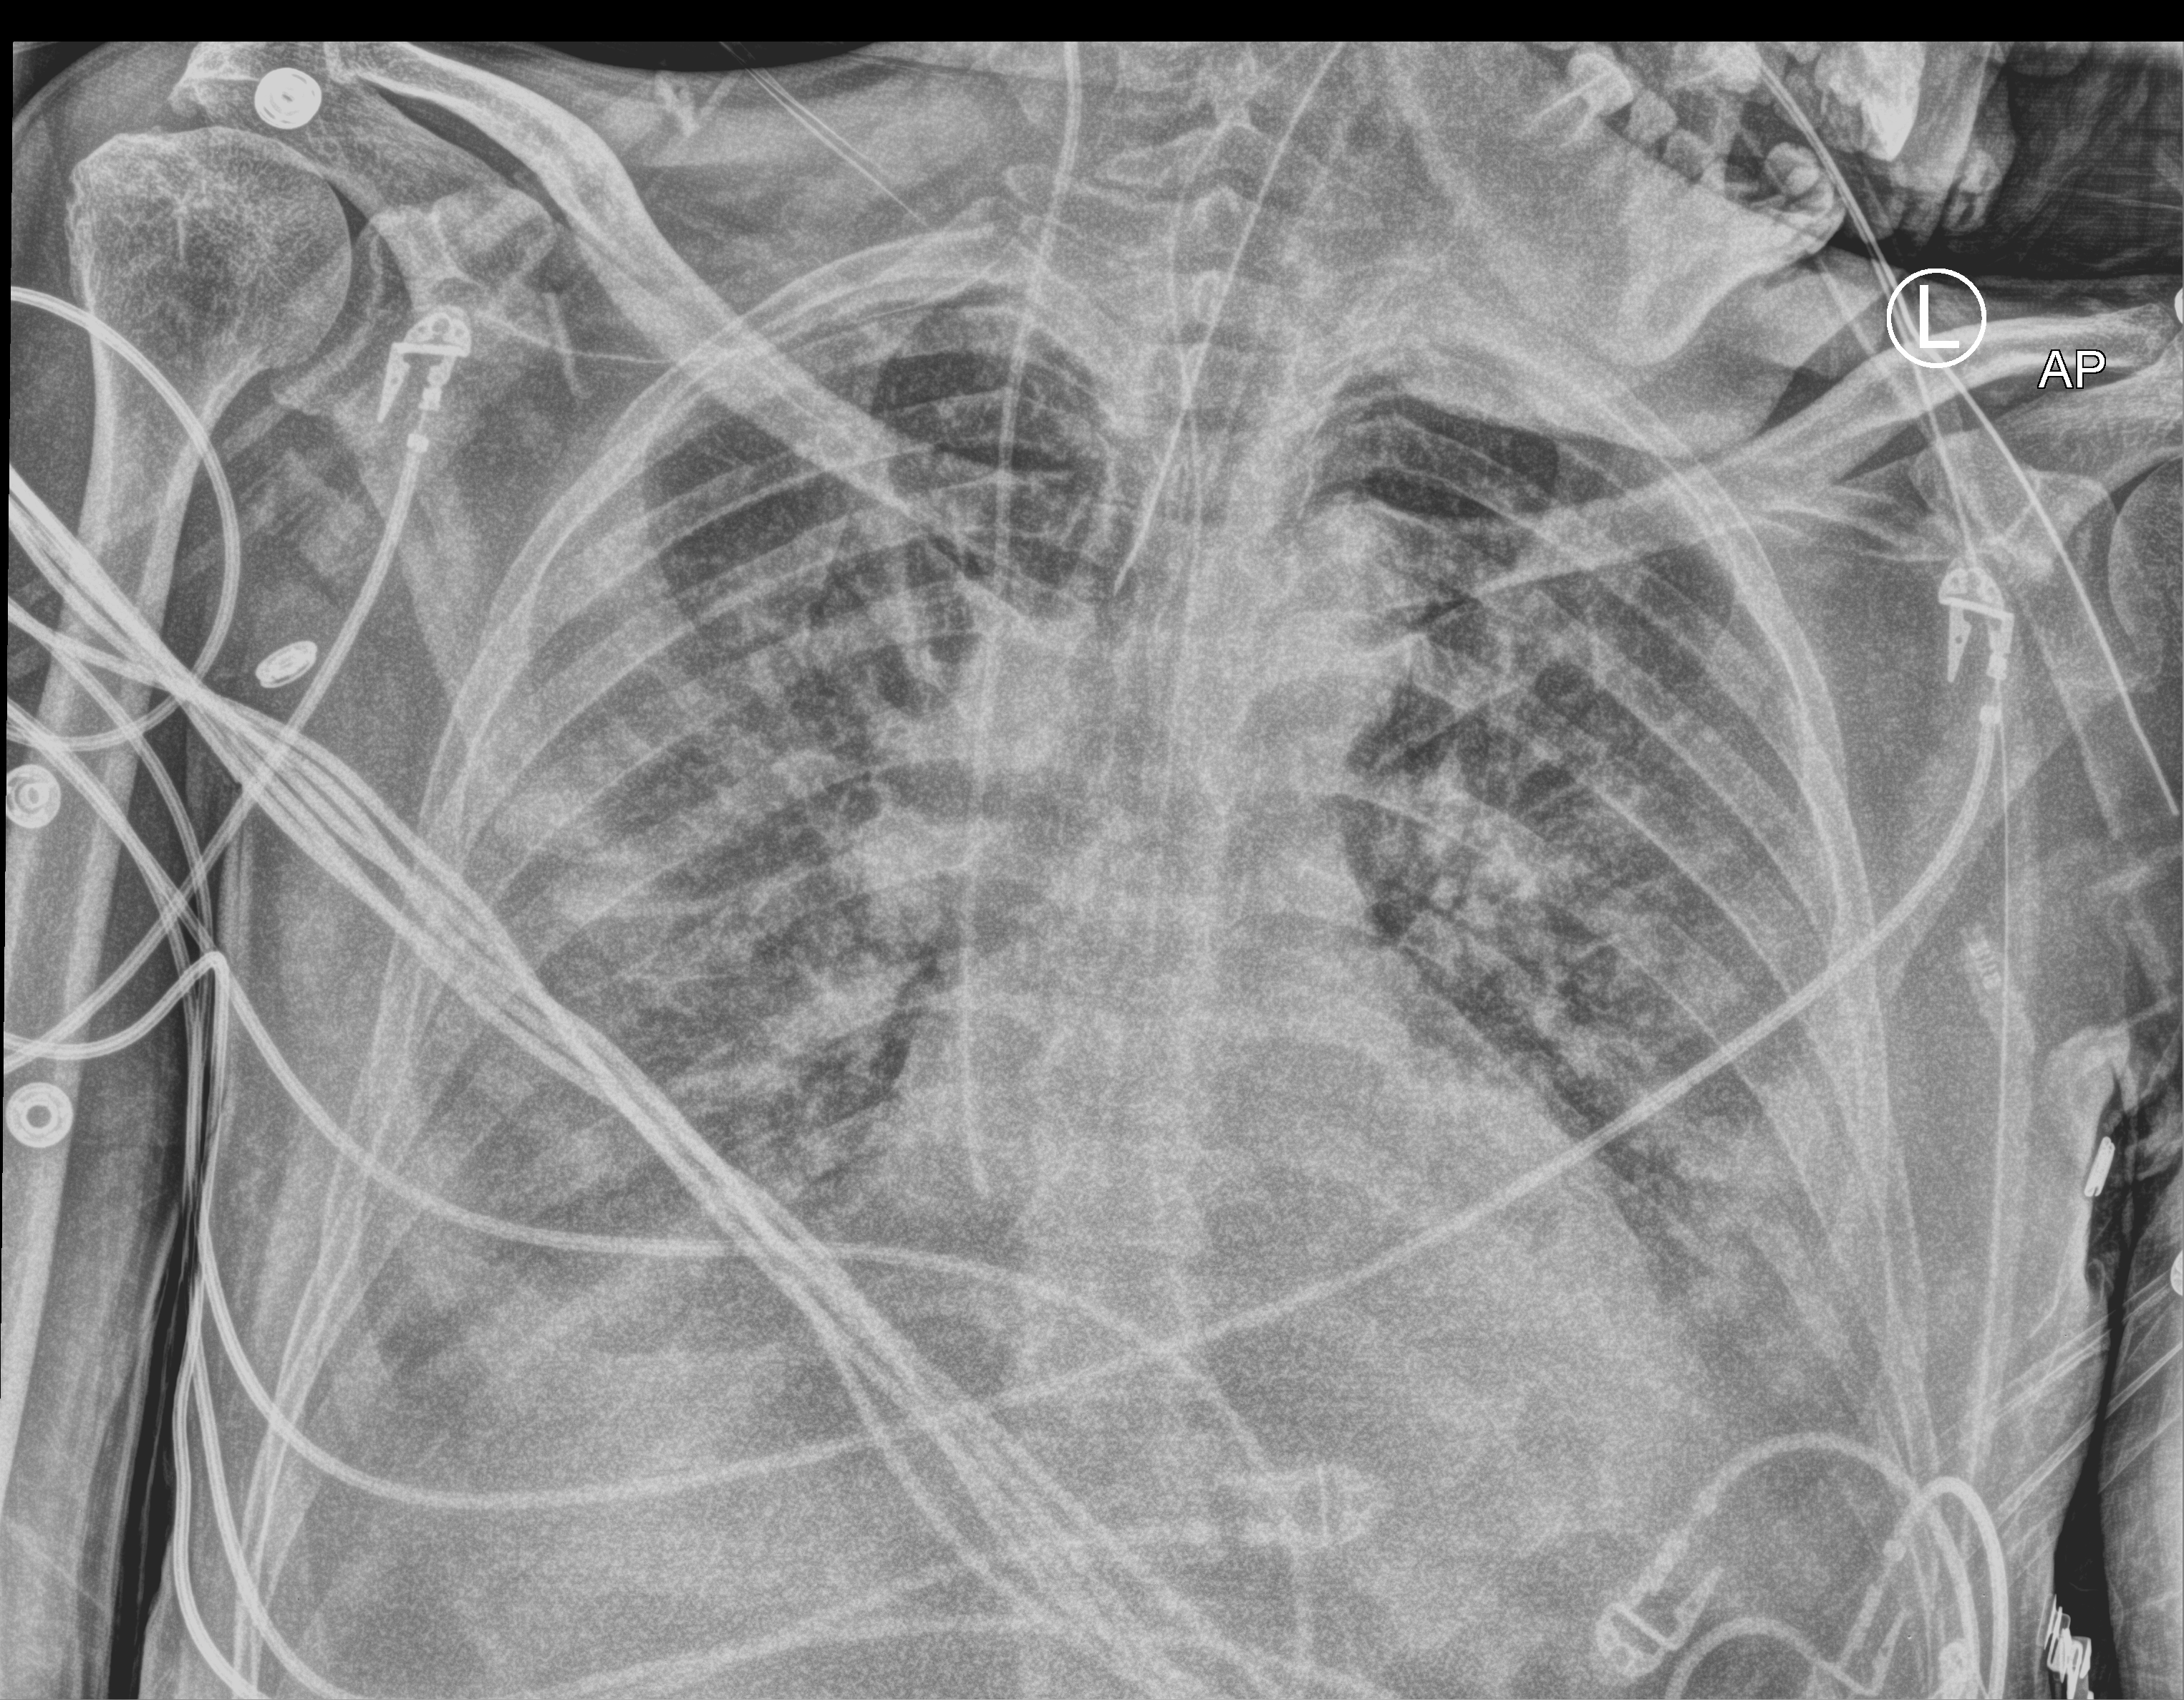
Bedside chest radiograph (computed radiography); anteroposterior (AP) projection. Male patient hospitalised with COVID-19, age 18–59 years.
From the hospital-stay record, not from the radiograph (when in the stay this image was taken is not recorded): admitted to intensive care during this hospital stay: yes; other chronic lung disease (admission record): no.